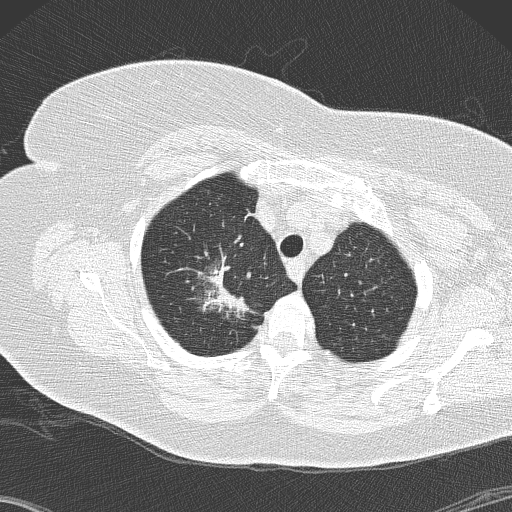
Axial slice from a low-dose chest CT screening exam. Second annual screen. Lung window (W 1500 / L -600 HU). 2 mm slice thickness. Lung (sharp) reconstruction kernel (B50f). Slice 26 of 146 in the series. Female, age 72 years at enrolment. Former smoker at enrolment.
Lesion marked by an expert reader, bounding box (x1, y1, x2, y2) in pixels: (181, 243, 261, 327). The screening reader recorded 4 non-calcified nodules or masses ≥4 mm on this exam (right lower lobe, right lower lobe, right lower lobe, right upper lobe); which of them this box marks is not recorded. Official screen result: positive, other. Lung cancer was diagnosed 52 days after this screen: bronchiolo-alveolar adenocarcinoma, NOS, right upper lobe, stage IIIB (AJCC 6th edition), 45 mm at pathology.